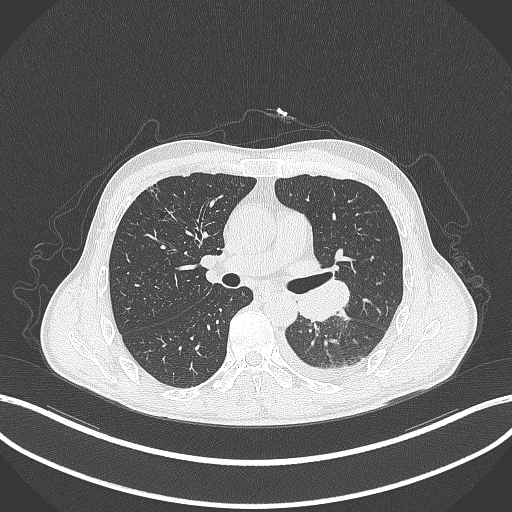
Chest CT, one axial slice; position 186 of 295 along the scan axis; lung window (W 1500 / L -600 HU); 1 mm slice thickness; 512 × 512 image matrix. Male patient, age 47 years. From the clinical record (not read from this slice): clinical TNM (as recorded): T3 N1 M1c; histopathological grade: G3.
Outlined on this slice (rectangle marked by the reading radiologist):
- lung tumour (recorded histology: small cell carcinoma): bounding box <298,276,351,321> (left, top, right, bottom; pixels)